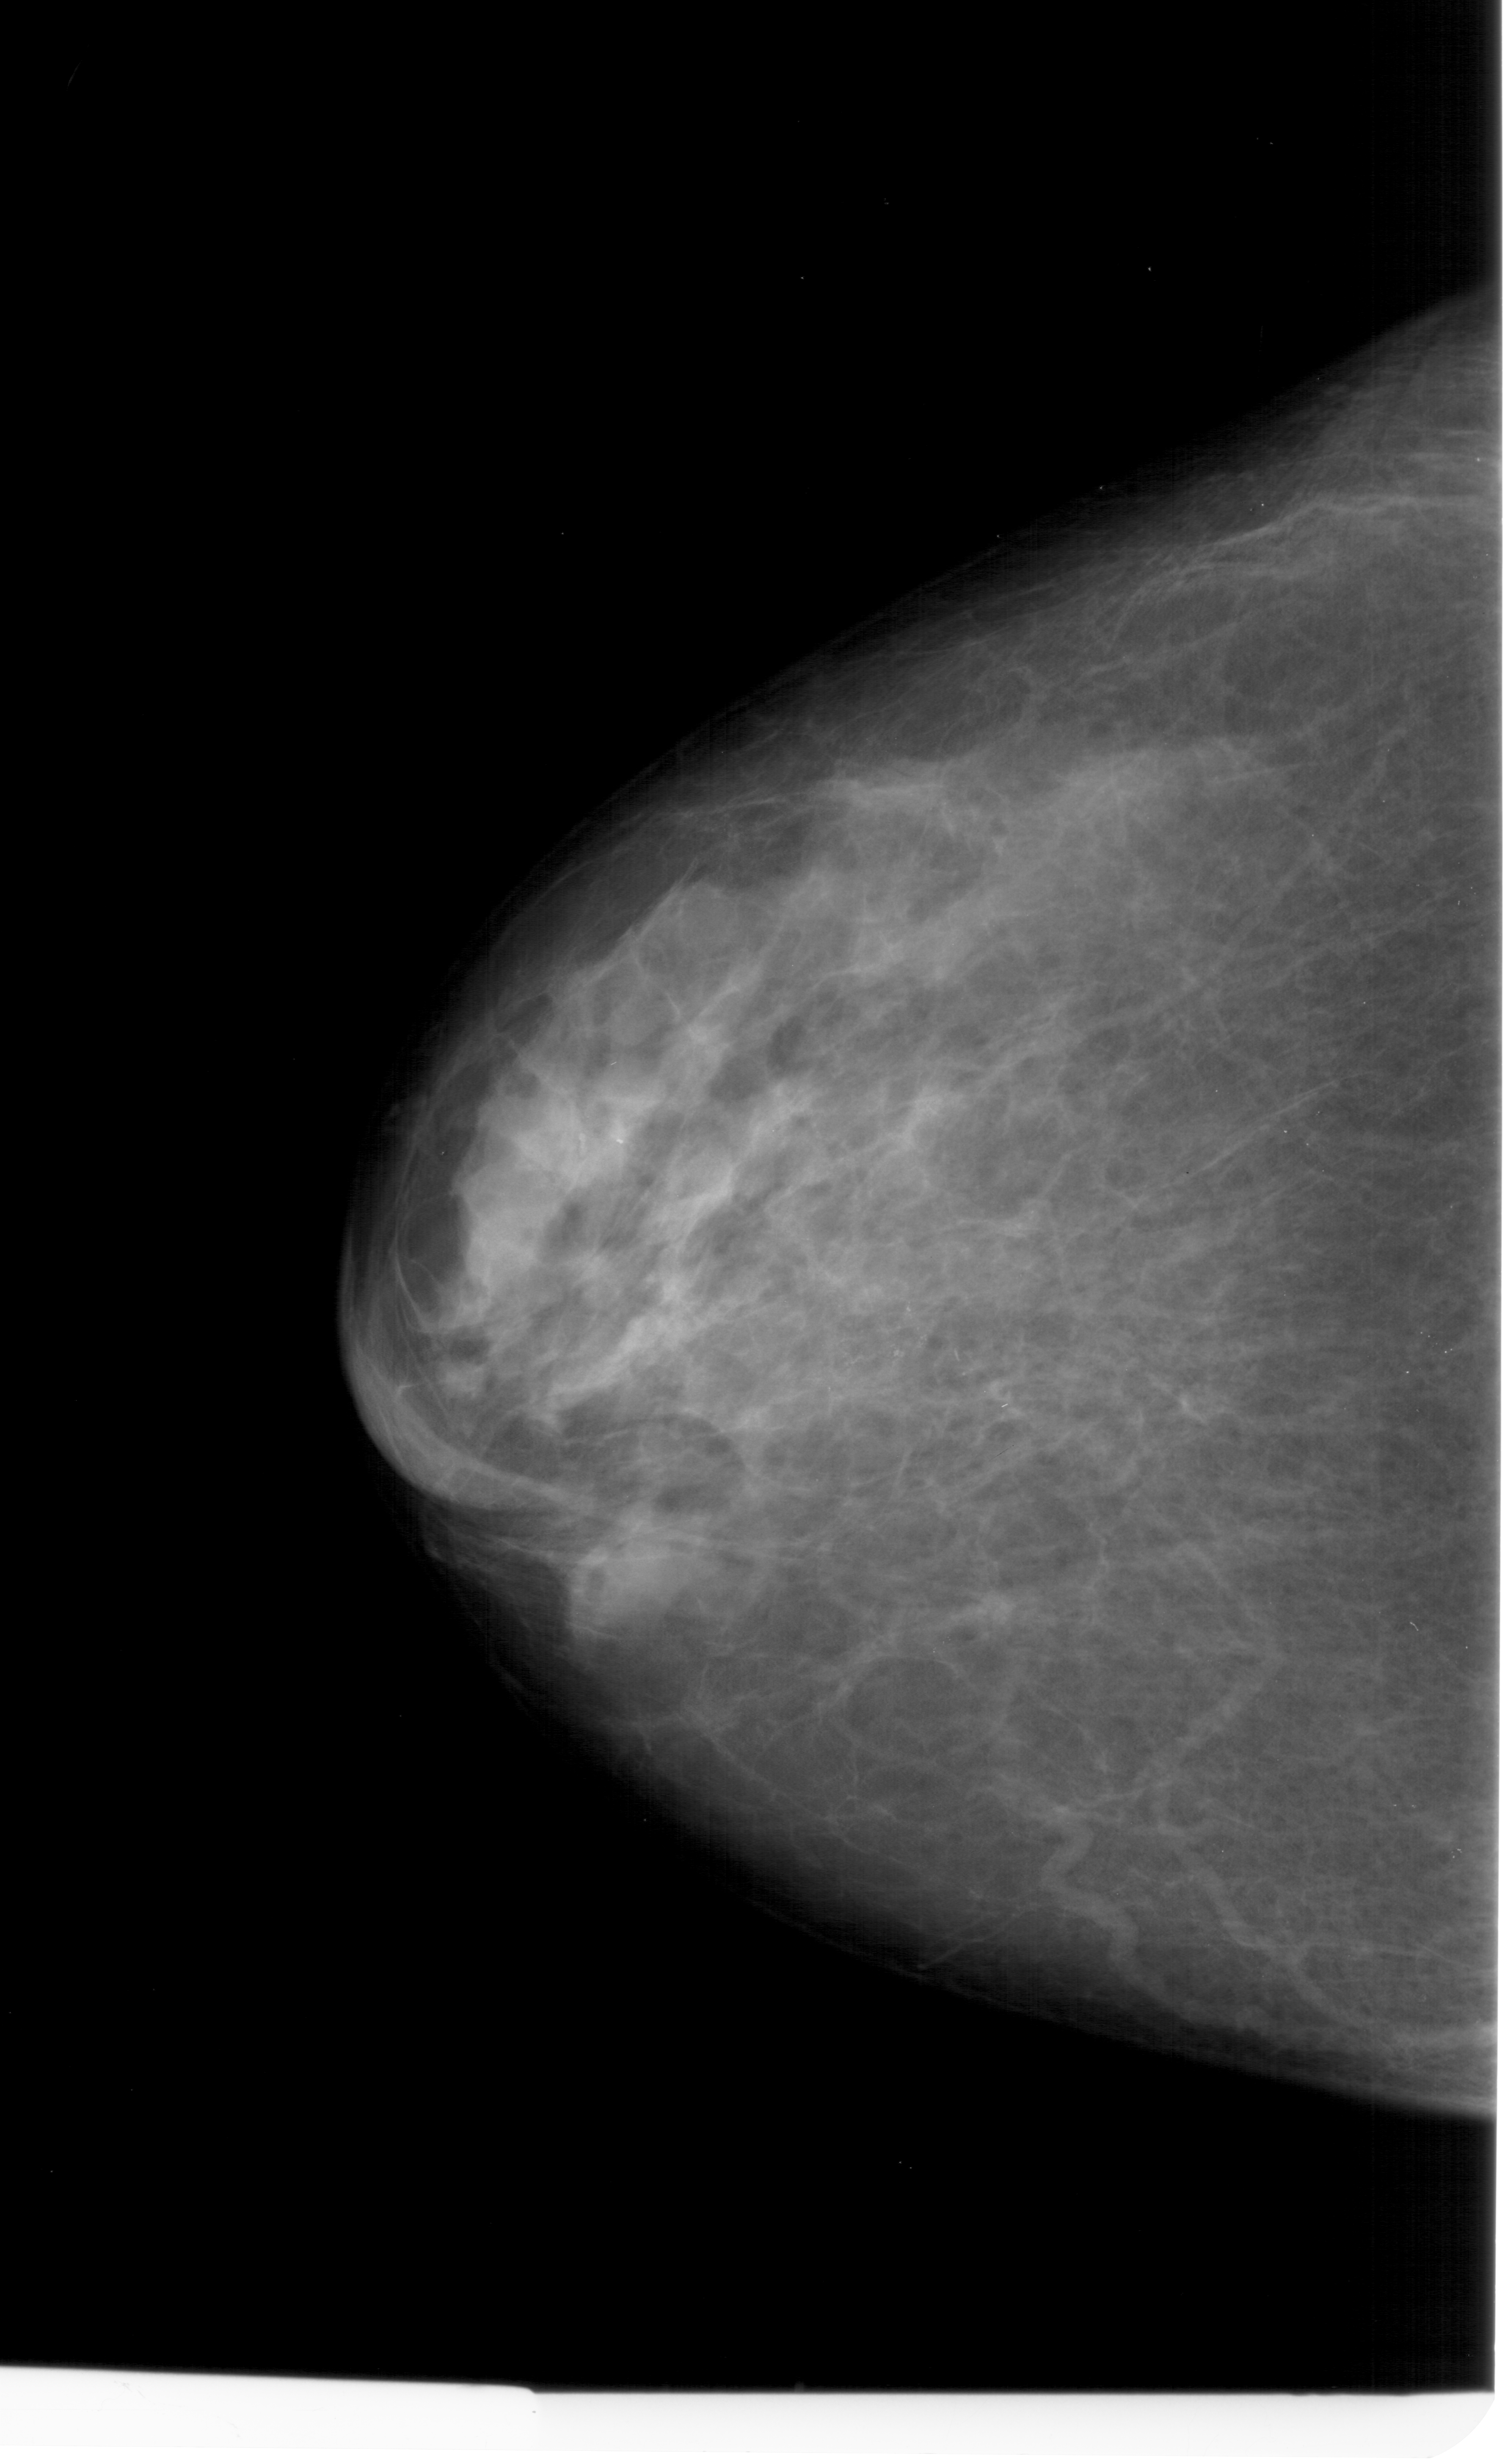
Digitized screen-film mammogram, left breast, CC view.
- Abnormality record for this image: calcifications, morphology pleomorphic, distribution clustered; BI-RADS assessment category 4; pathology result (as recorded, not read from the image): benign.